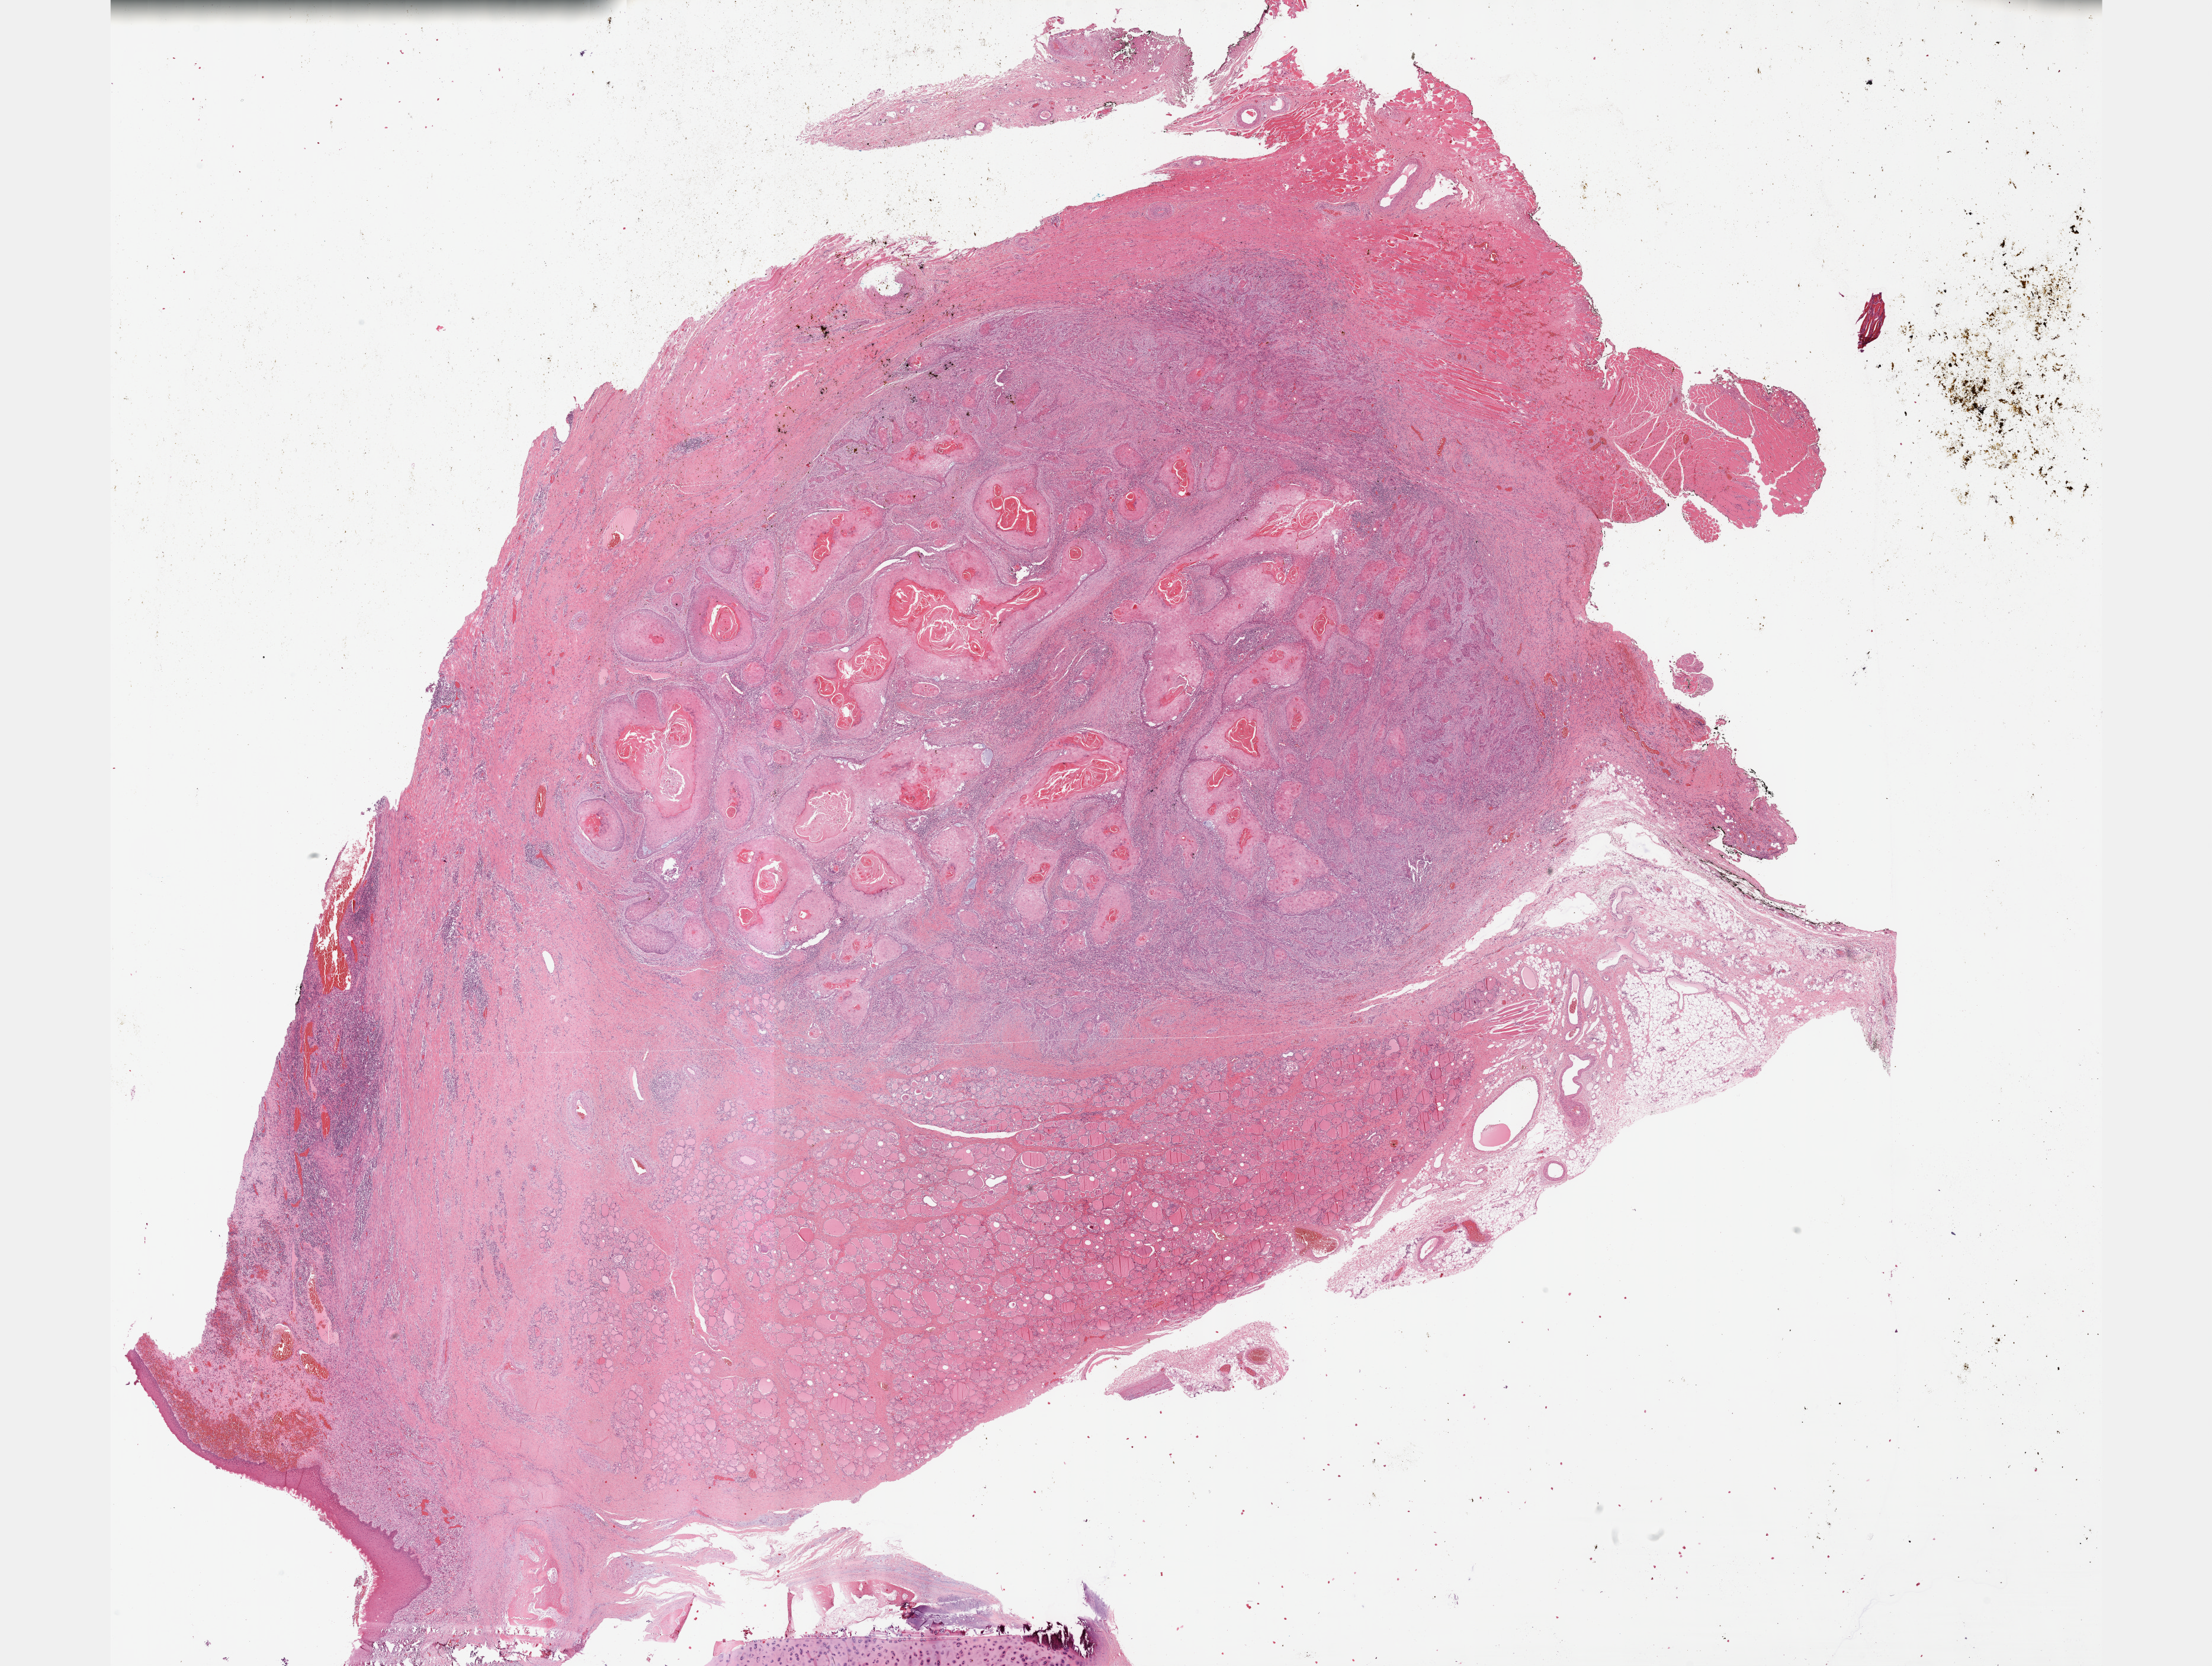
H&E-stained whole-slide image — whole scanned area (about 30.2 x 22.7 mm) shown as a low-resolution overview; FFPE section; primary tumour sample from the head and neck. Patient: male, age at initial diagnosis 68 years. Histologic grade: G1 (well differentiated).
Laterality: midline. AJCC pathologic stage: IVA. TNM: T4a N0 M0. Pathologic diagnosis: Squamous cell carcinoma, keratinizing, NOS (larynx, NOS).